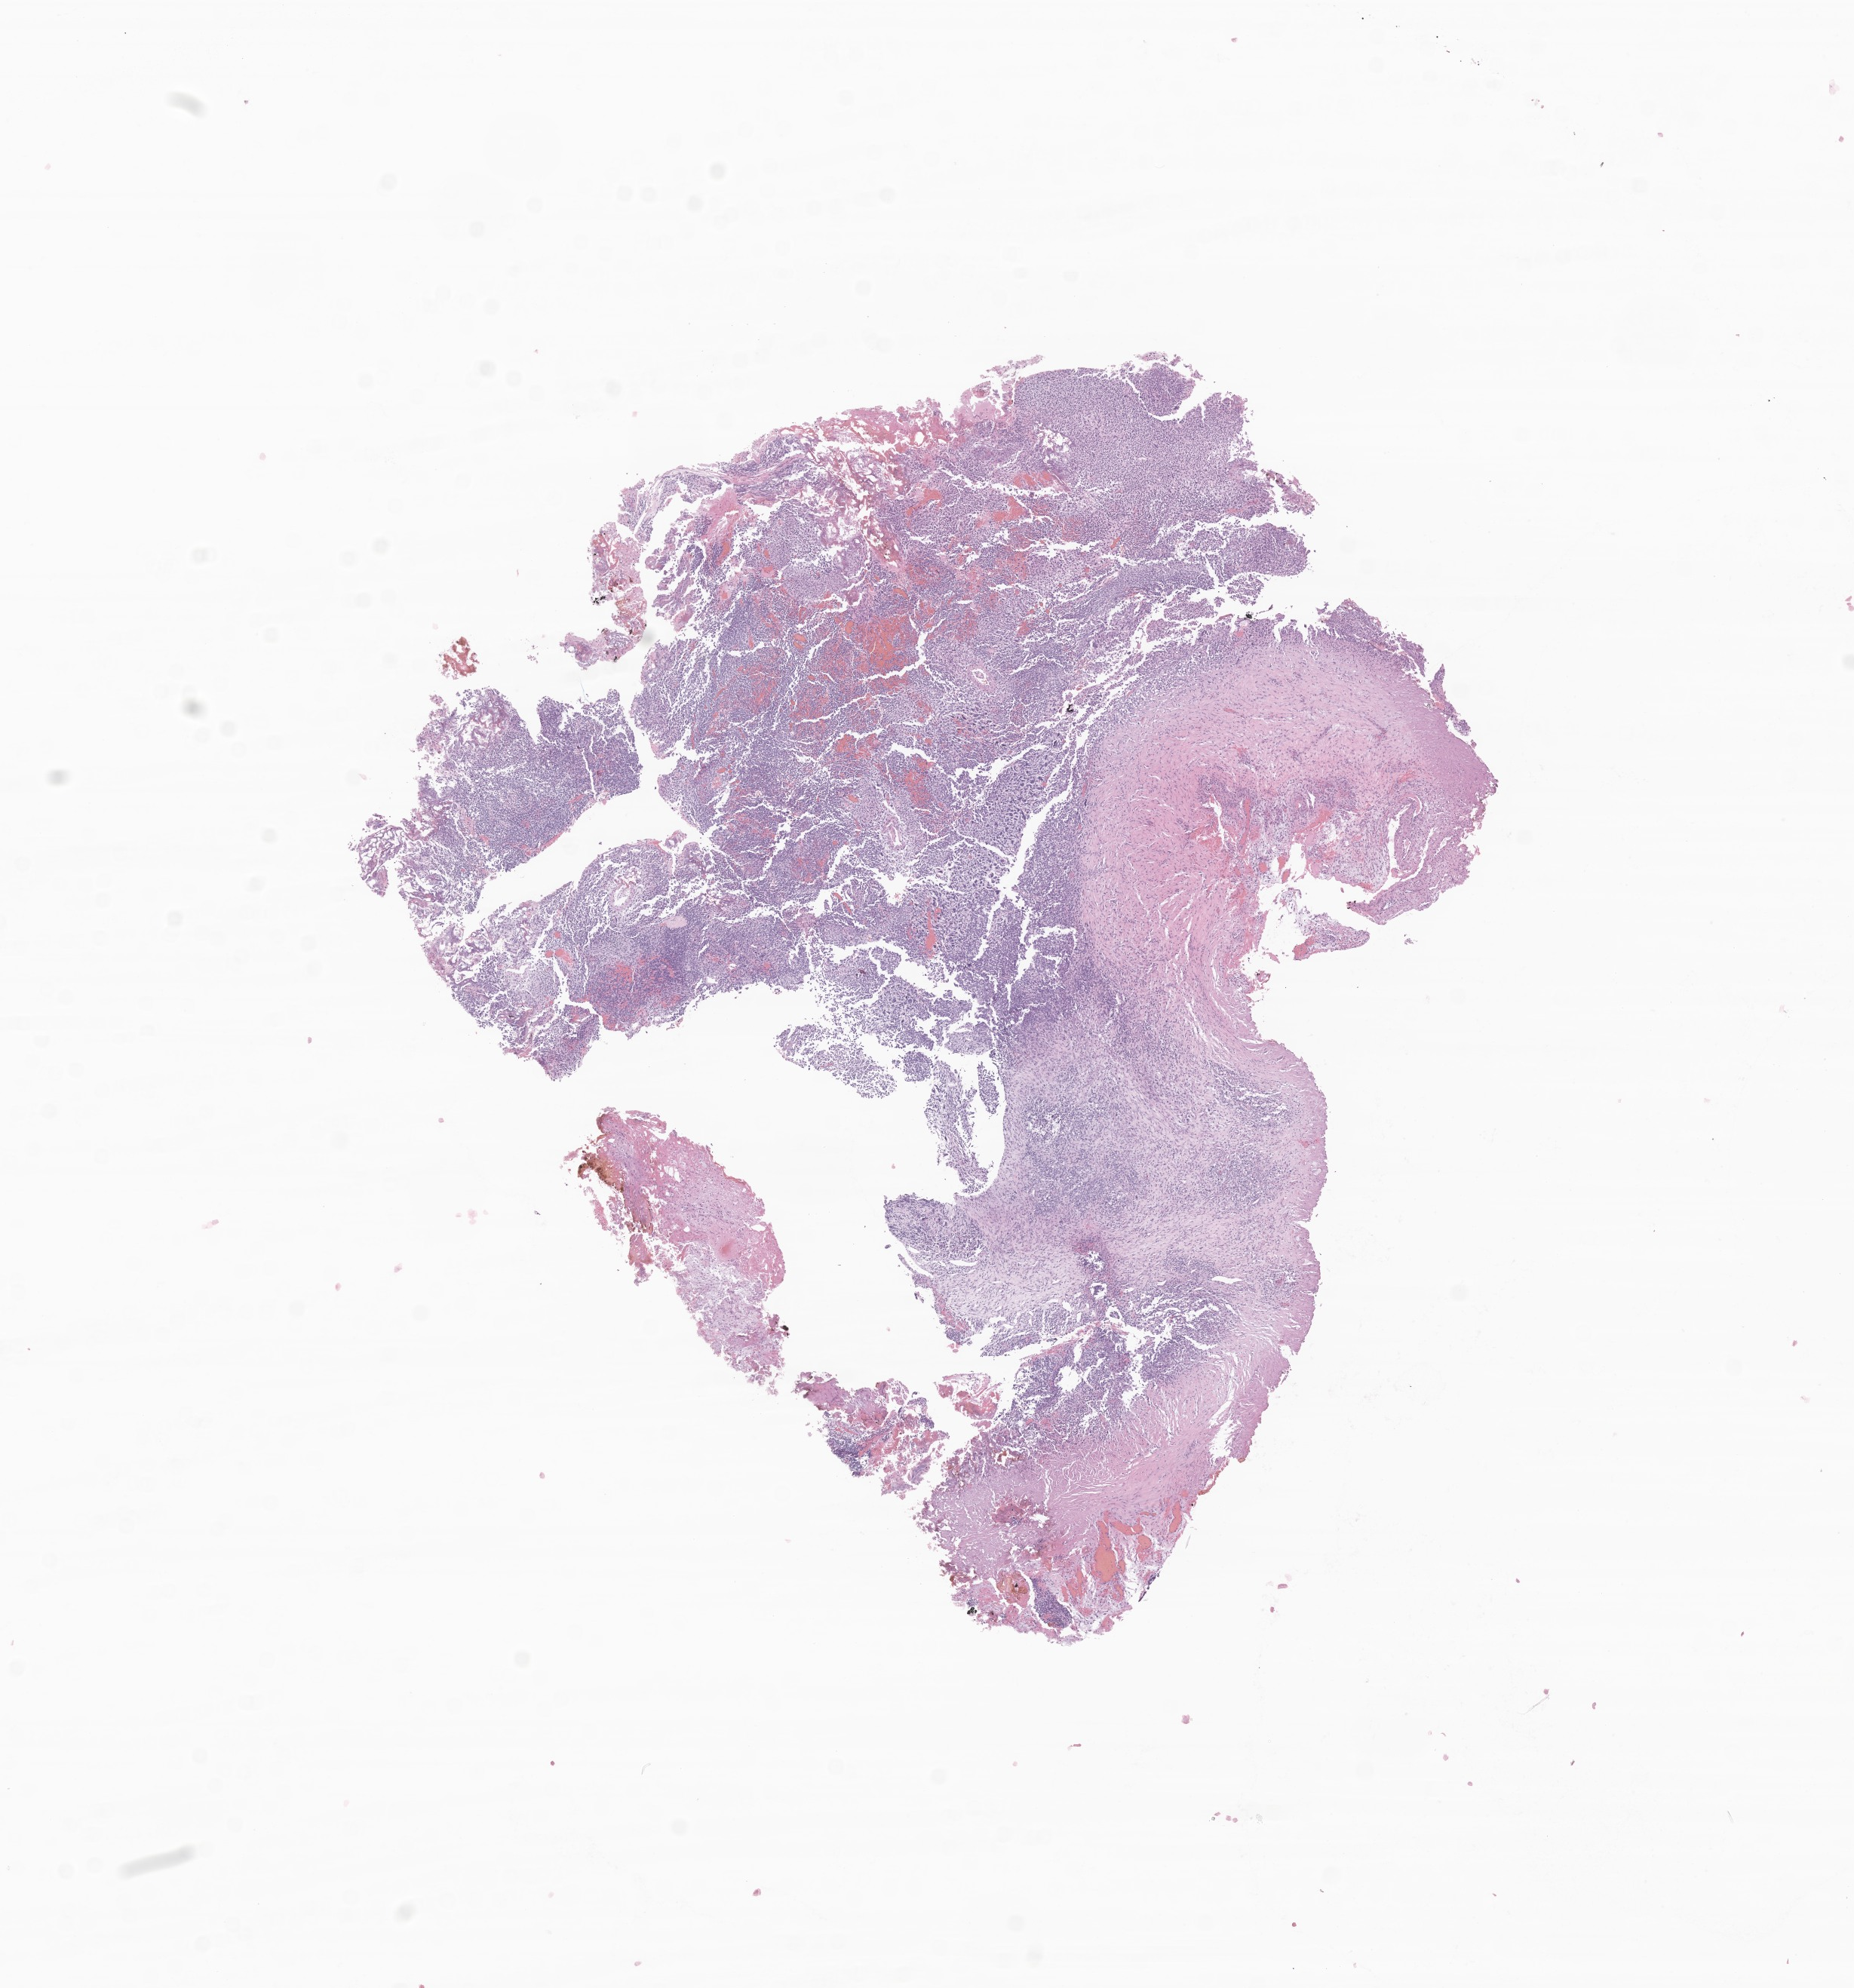
Whole-slide image, hematoxylin and eosin (H&E) stain of tumor tissue from the lung, low-resolution overview of the scanned area, about 10.4 x 11.1 mm, formalin-fixed, paraffin-embedded (FFPE) tissue. Male patient, age 39 months (3 years 3 months).
* recorded diagnosis: Pleuropulmonary blastoma